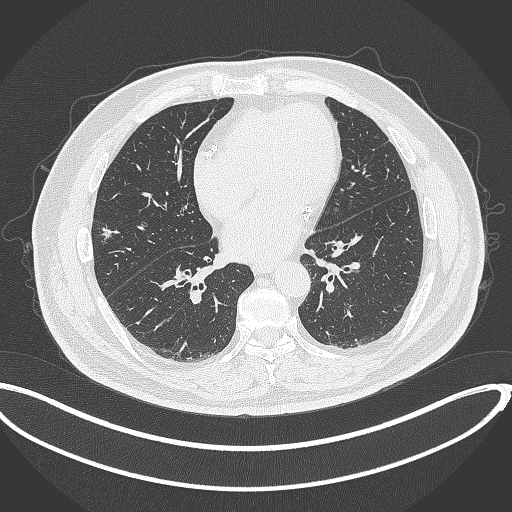
Chest CT, one axial slice. Slice 136 of 340 in the series (ordered by position). 120 kVp. Lung window (W 1500 / L -600 HU). 1 mm slice thickness. 512 × 512 image matrix, field of view 427 × 427 mm. Patient: male, 68 years. From the clinical record (not read from this slice): clinical TNM (as recorded): T1c N0 M0.
Annotated regions visible in this slice (bounding box drawn by a radiologist):
- lung tumour (recorded histology: adenocarcinoma): bounding box (x1, y1, x2, y2) in pixels: (99, 224, 117, 240)